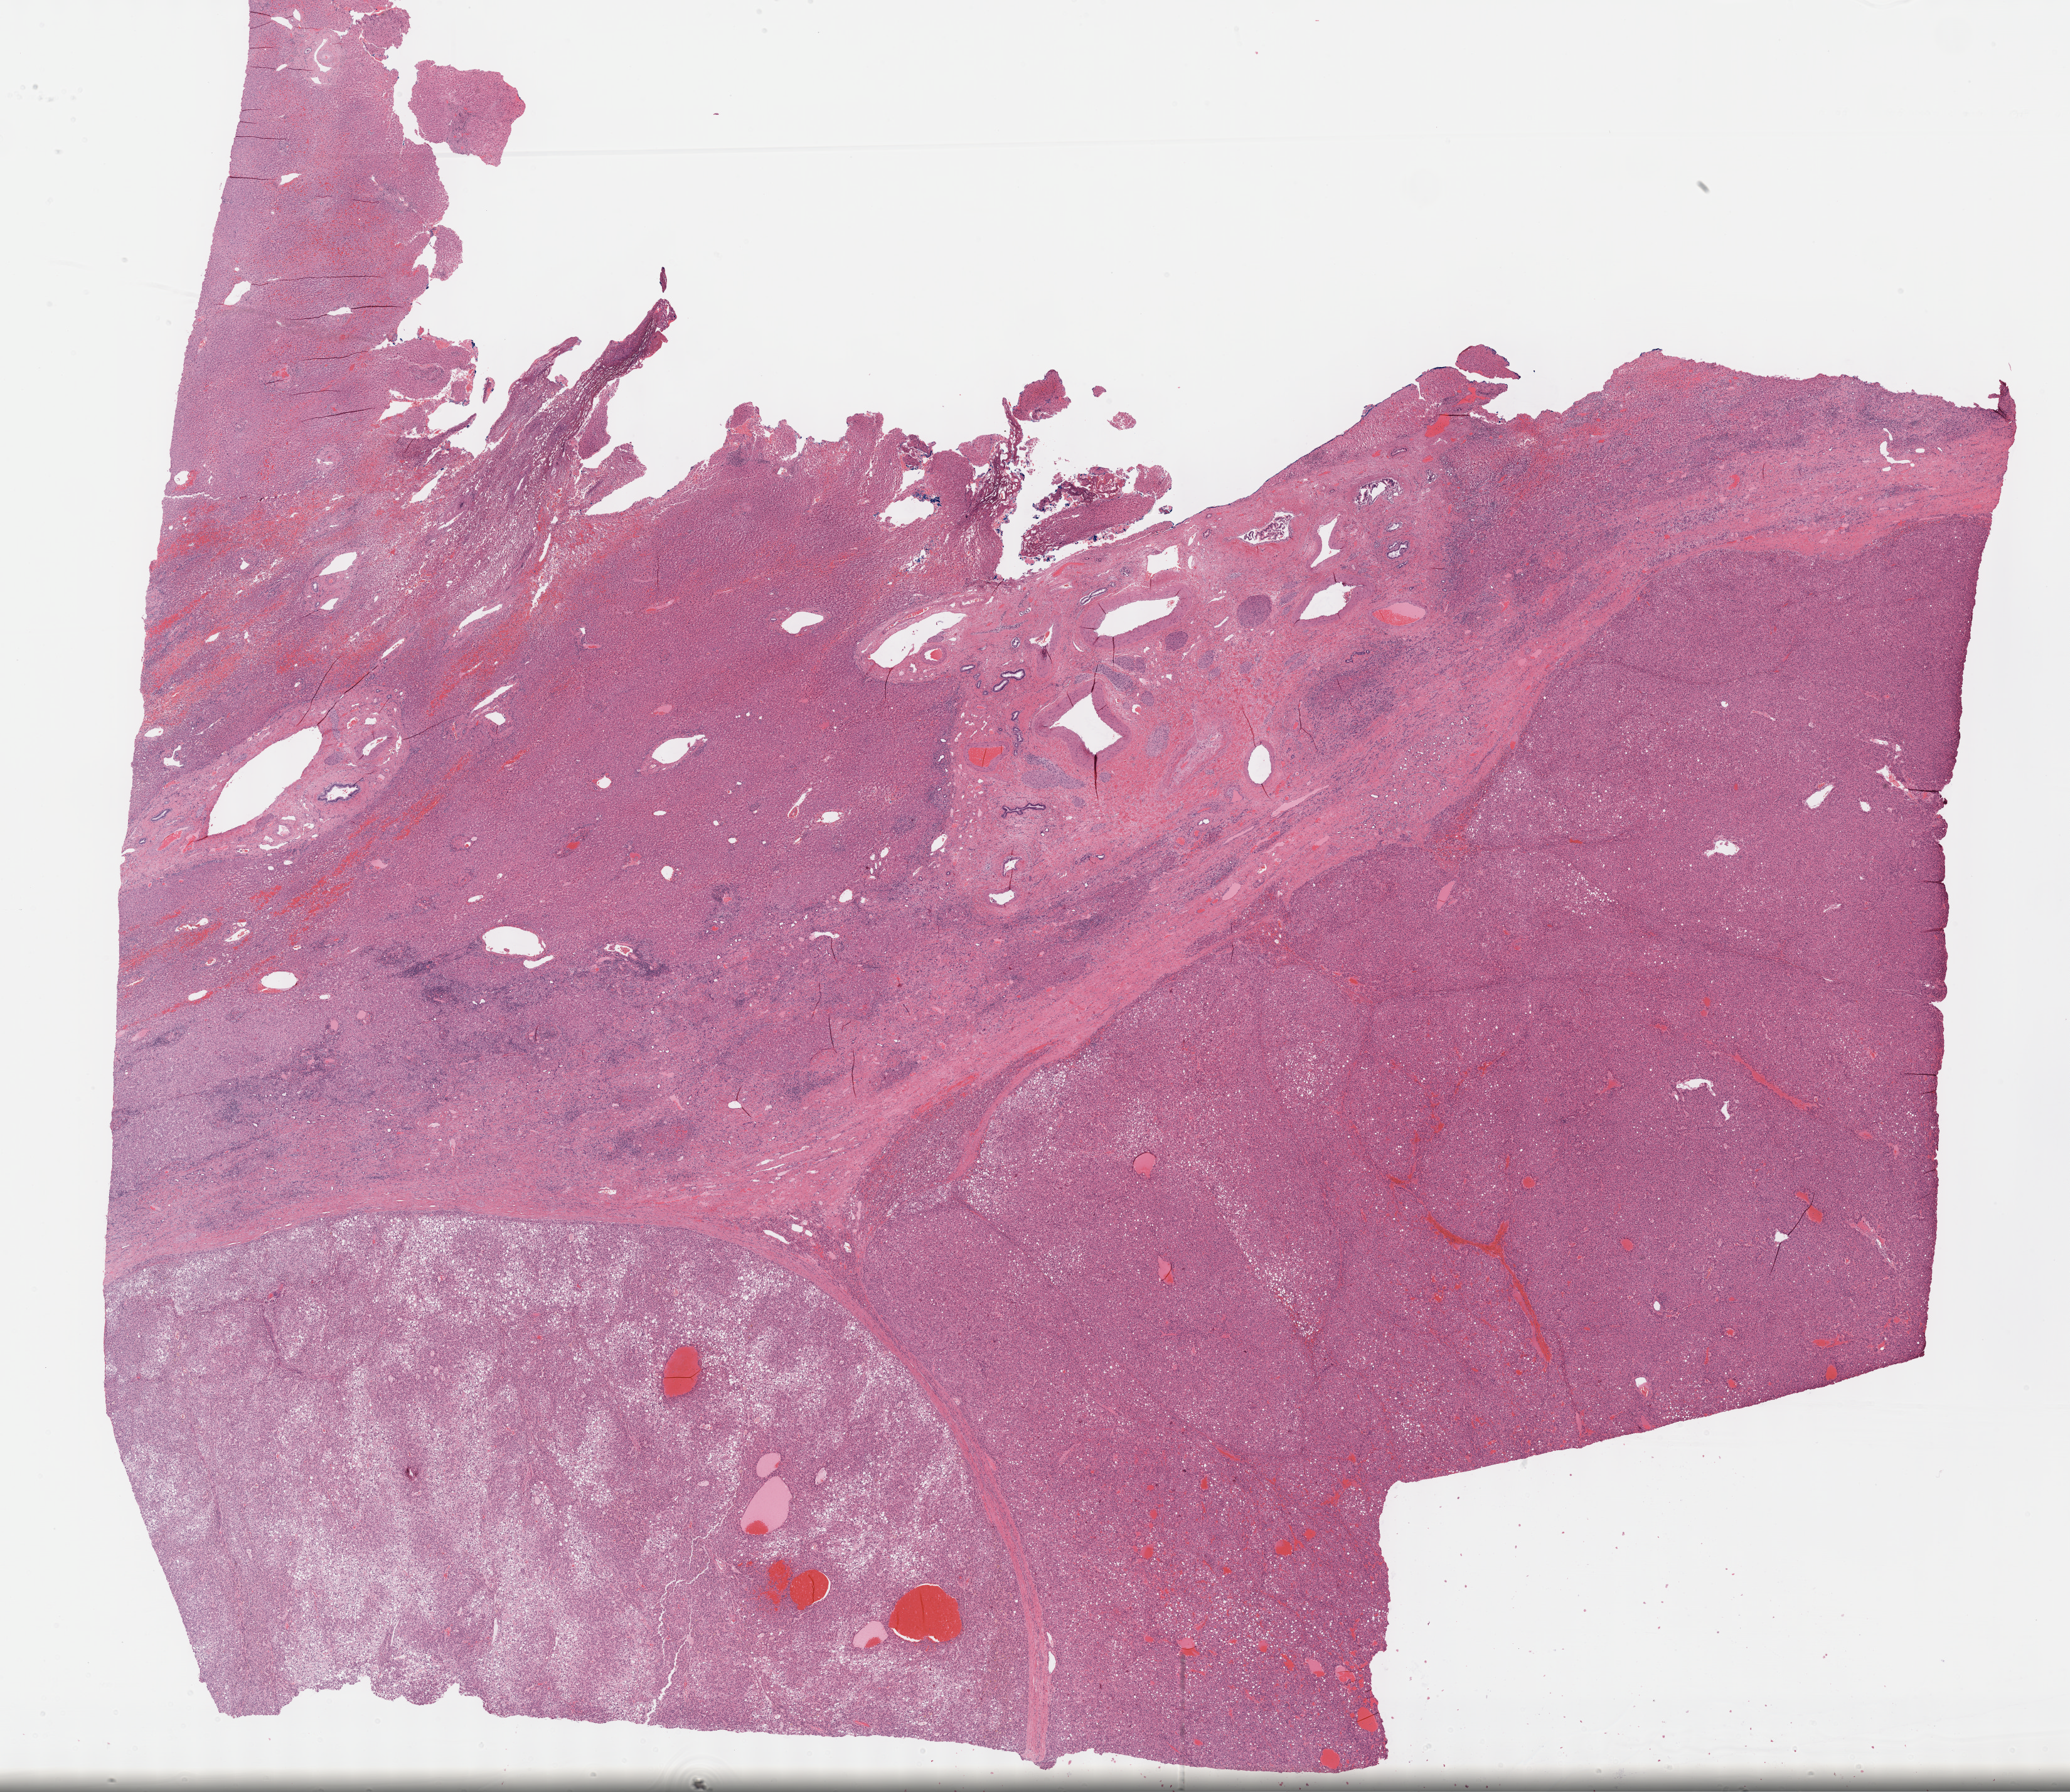
Digitized Hematoxylin and eosin (H&E) stained tissue section (whole slide), shown as a low-resolution overview of the whole scanned area (about 26.7 x 23.1 mm). Formalin-fixed paraffin-embedded (FFPE) diagnostic section. Primary tumour sample from the liver. Male, age 76 years at initial diagnosis. Histologic grade: G2 (moderately differentiated).
AJCC pathologic stage: I. Histologic diagnosis: Hepatocellular carcinoma, NOS.